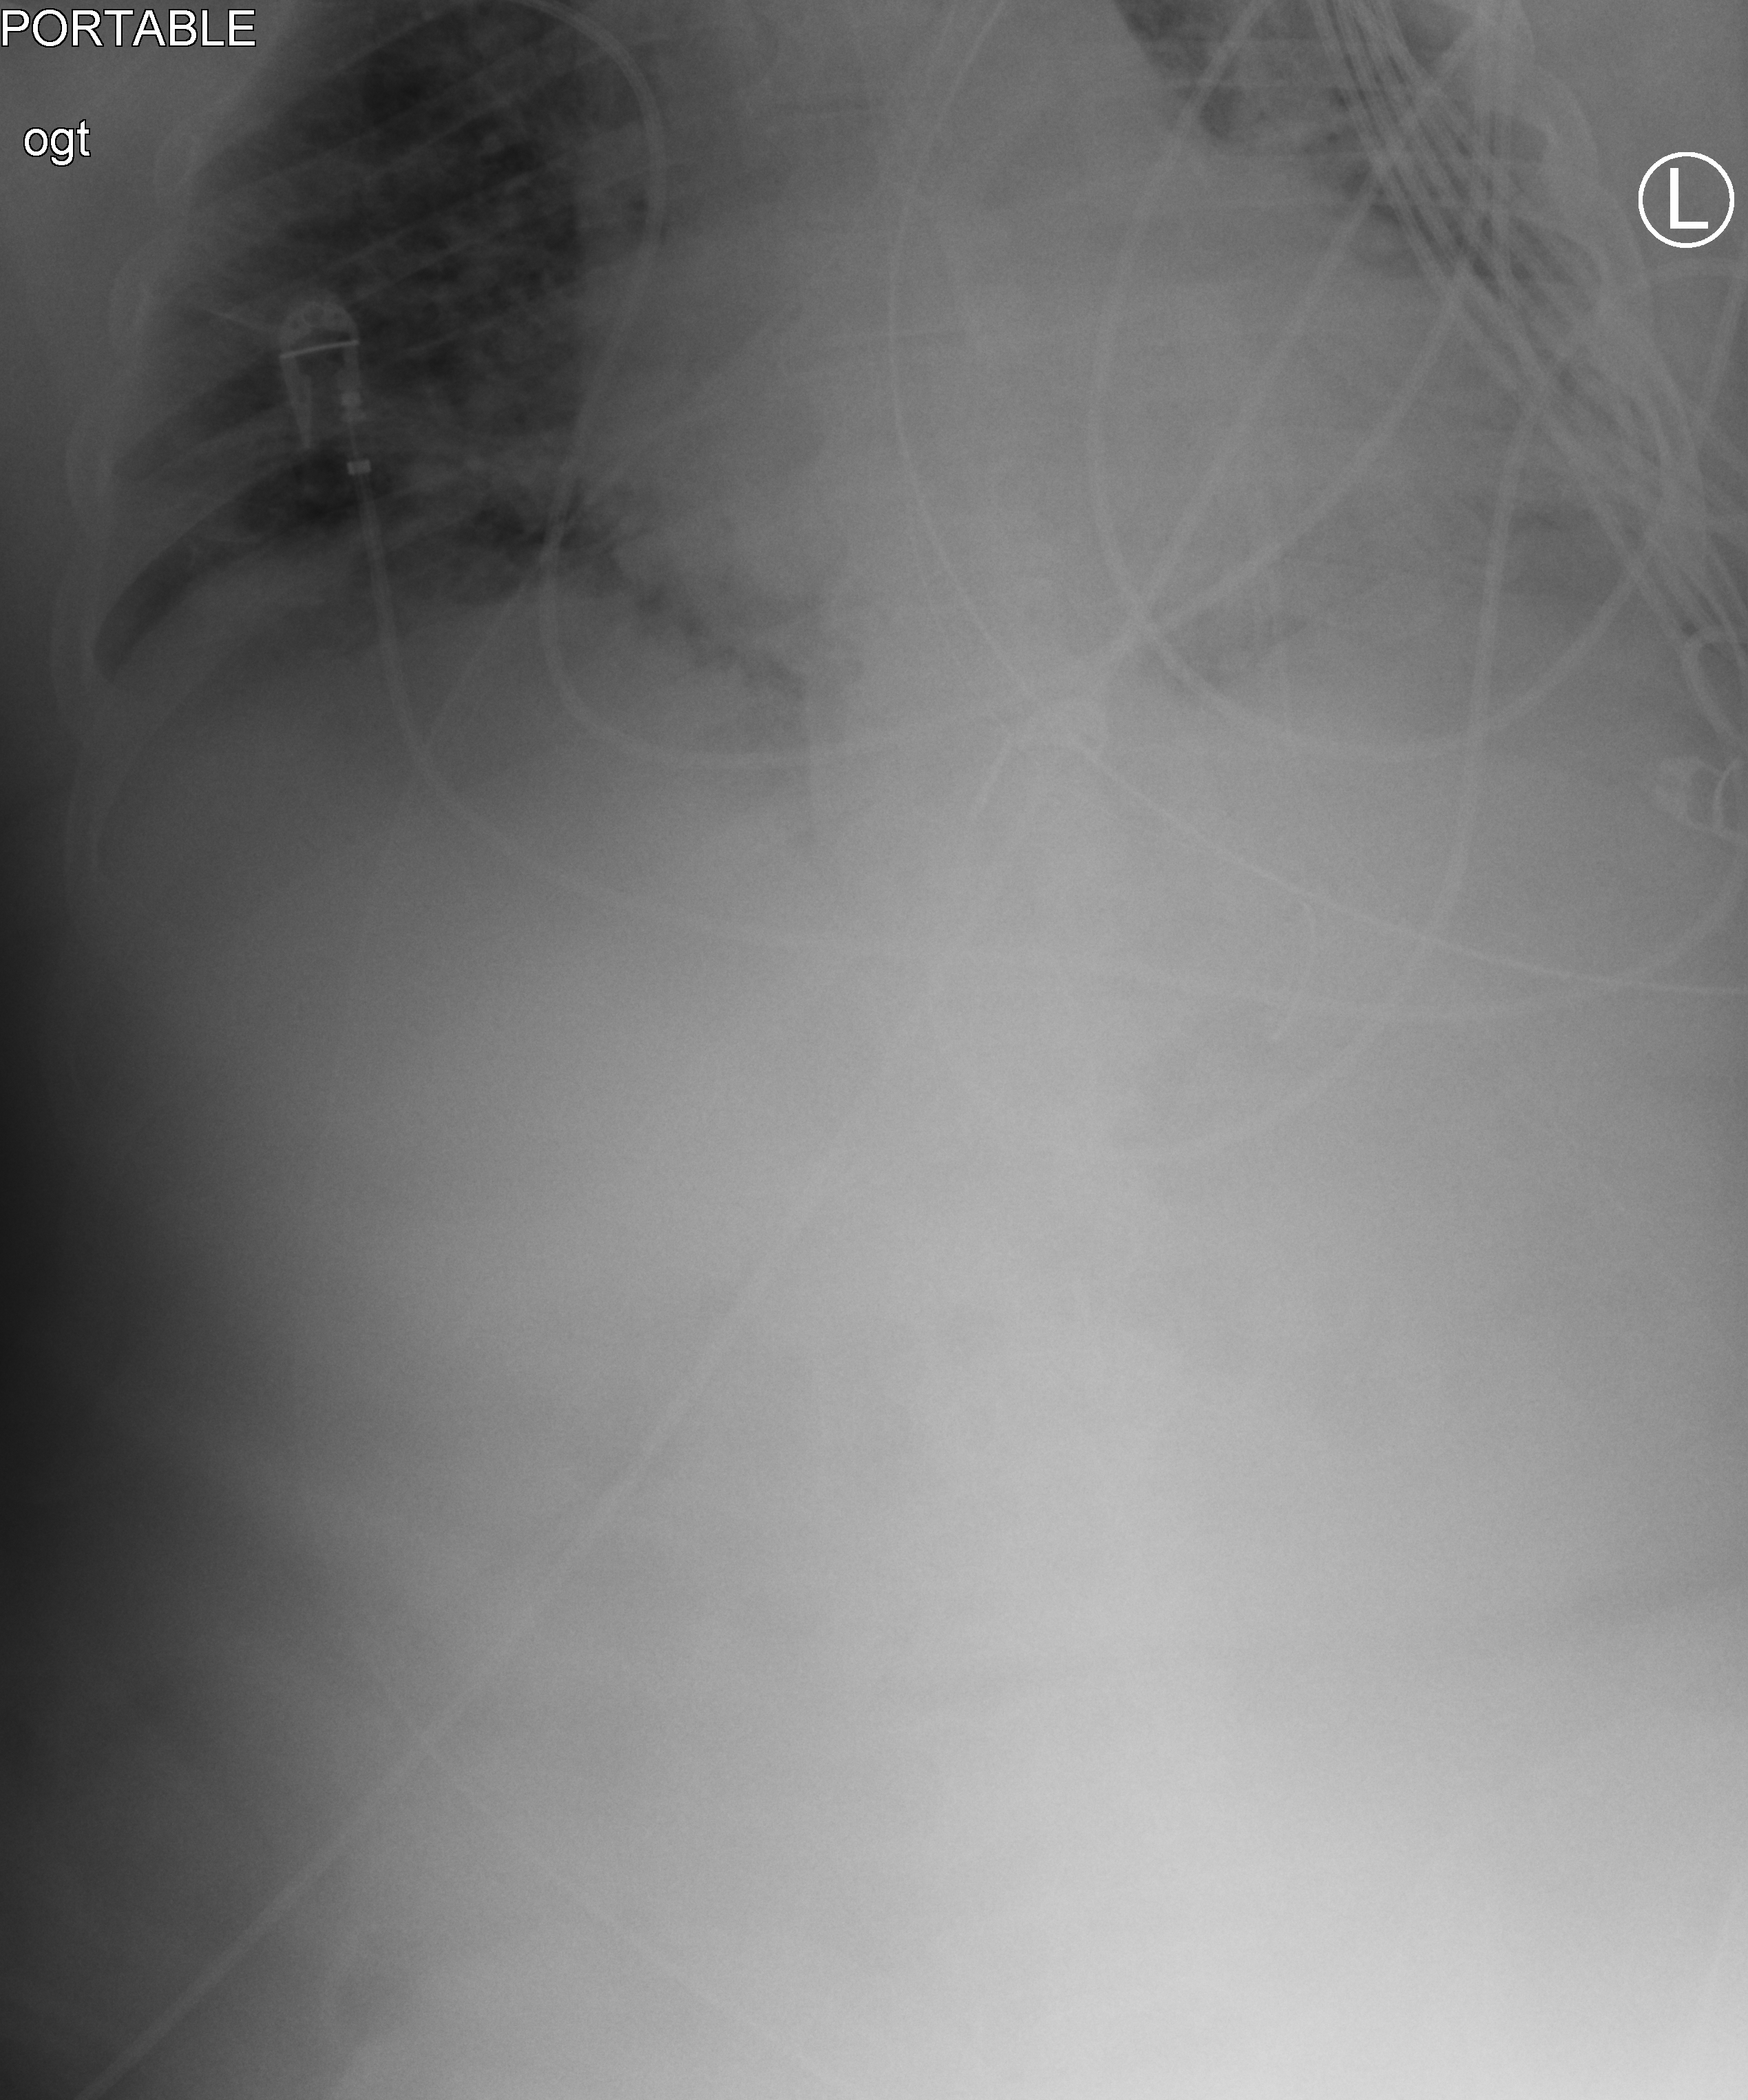
Chest X-ray (portable), anteroposterior (AP) projection. Patient hospitalised with COVID-19; male, aged 18–59 years.
Admission-level facts for this patient (not findings on this image; timing relative to this image not recorded):
- length of hospital stay: 28 days
- mechanically ventilated during this hospital stay: yes
- admitted to intensive care during this hospital stay: yes